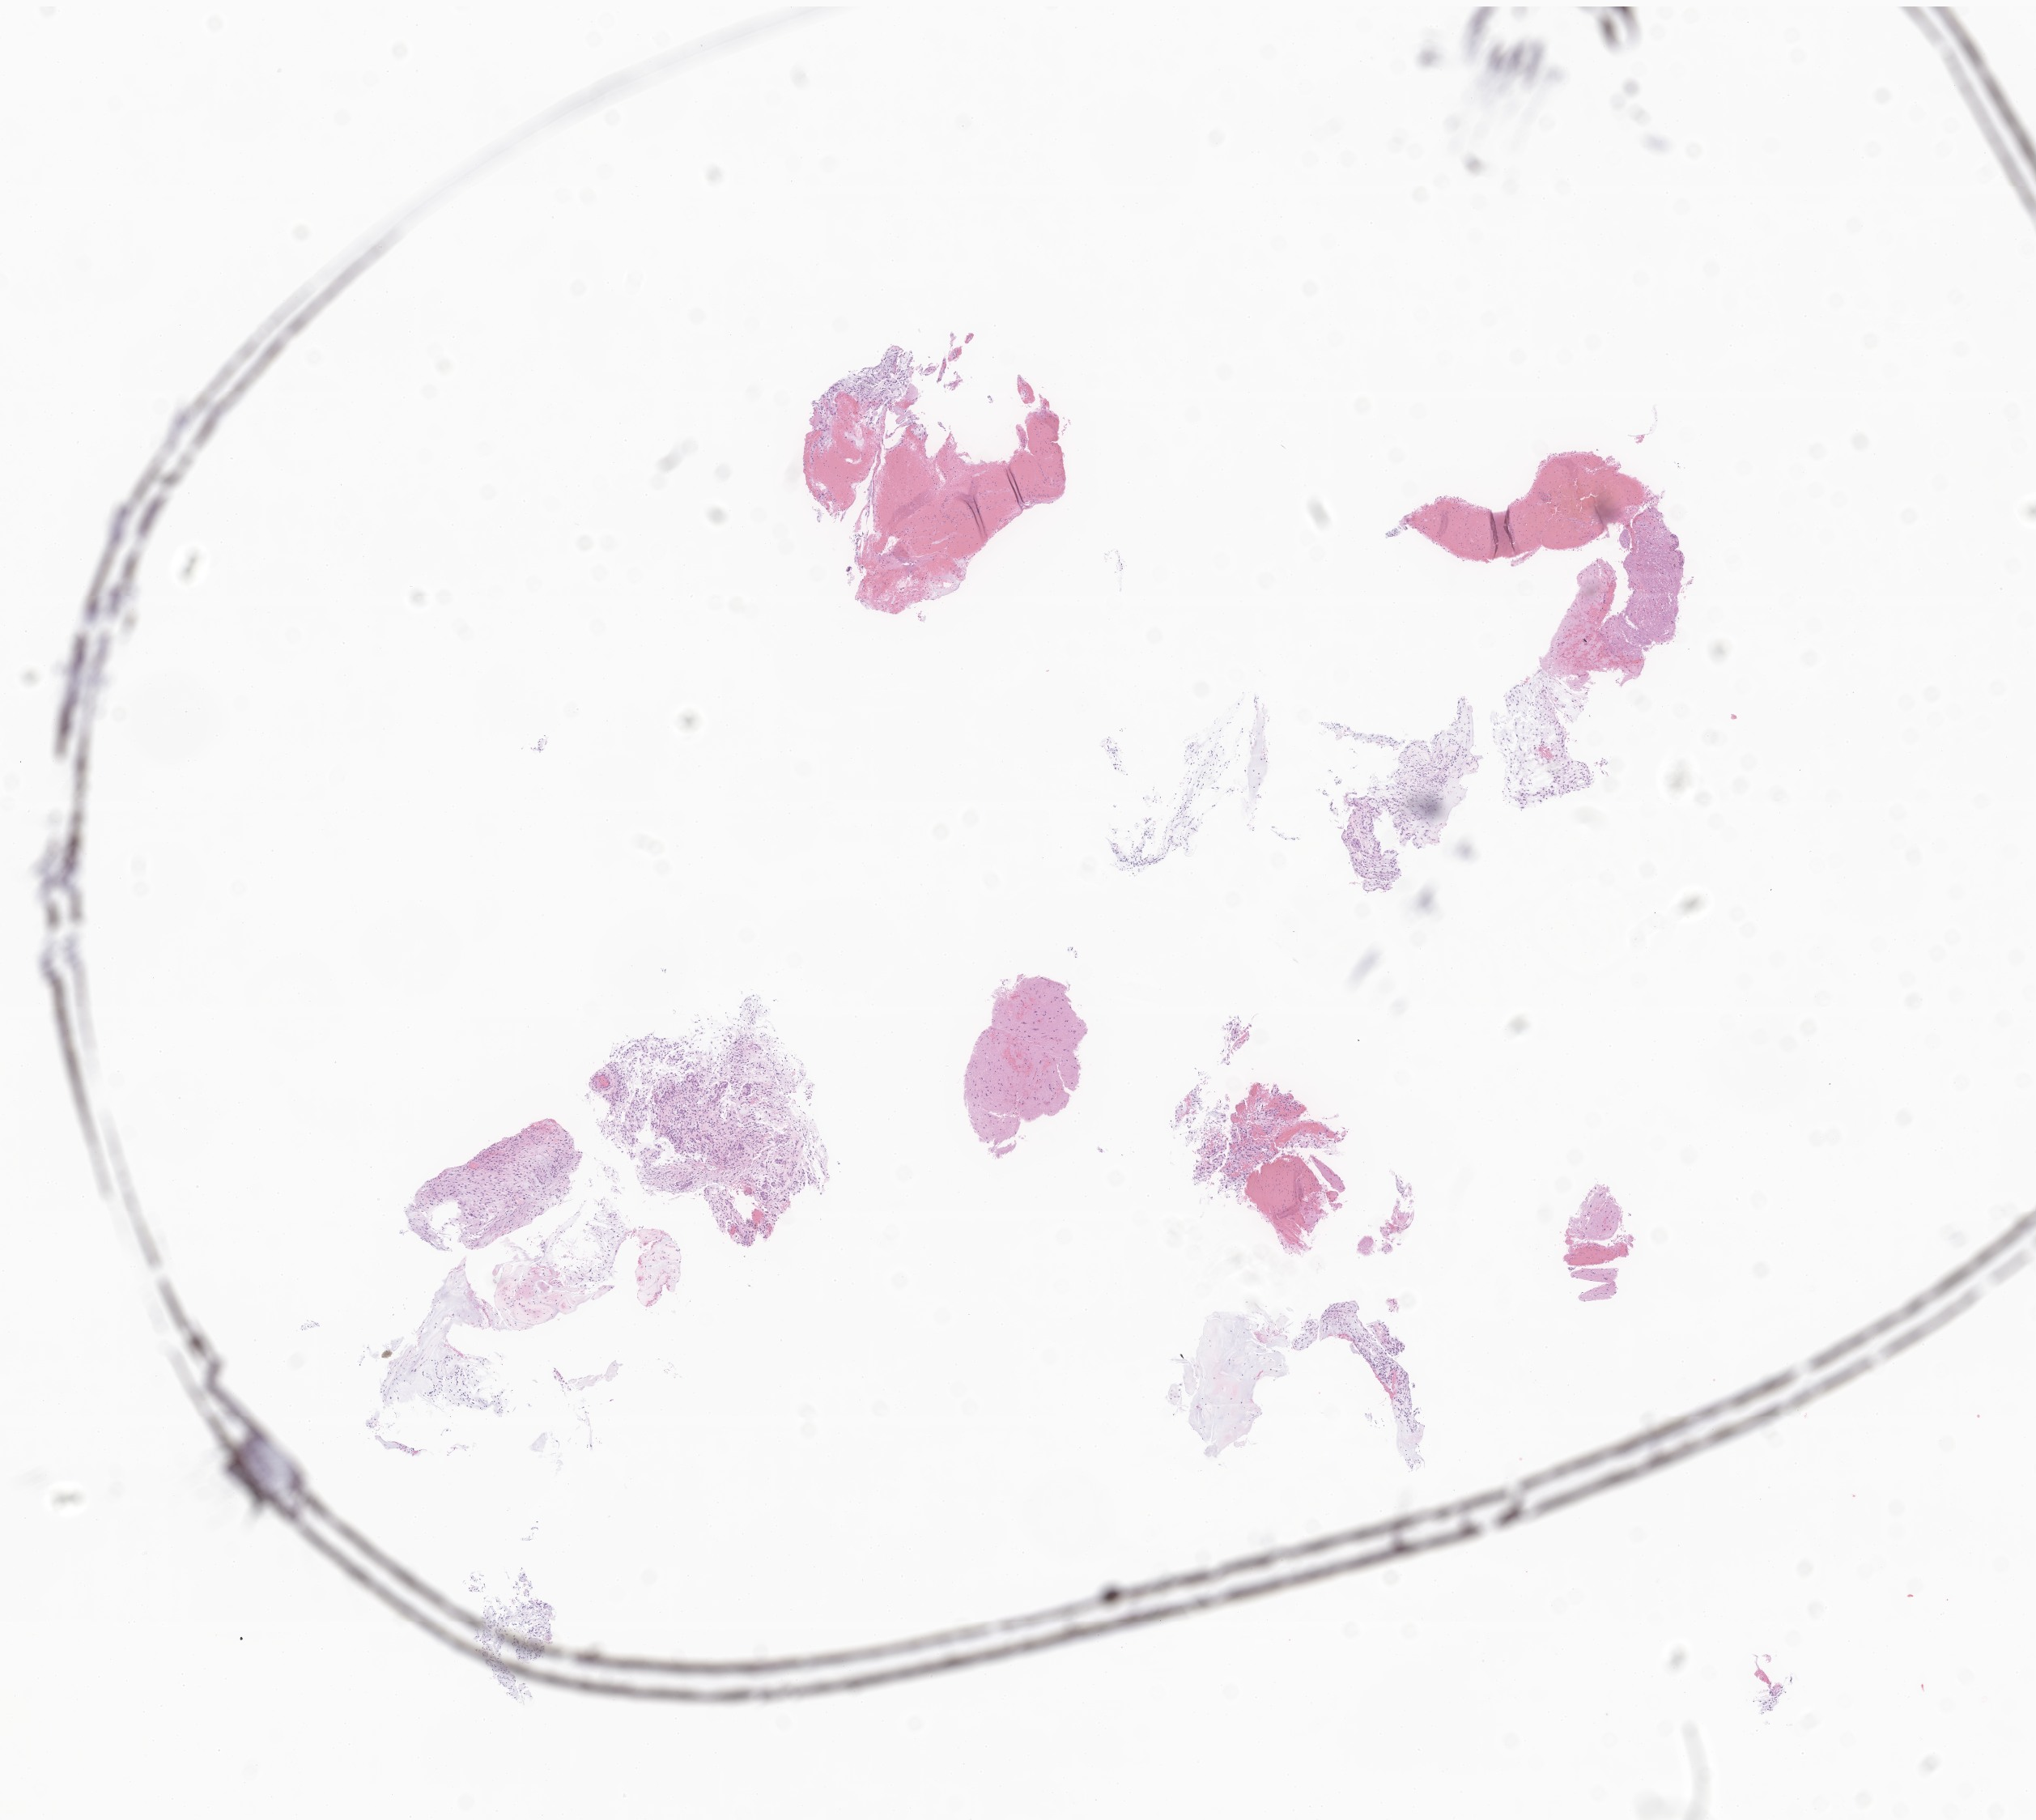
Digitized hematoxylin and eosin (H&E)-stained section of tumor tissue from the brain — a low-resolution overview of the entire scanned area, about 10.6 x 9.5 mm, formalin-fixed paraffin-embedded section. Patient male; age 173 months (14 years 5 months).
Diagnosis: Glioma, malignant.